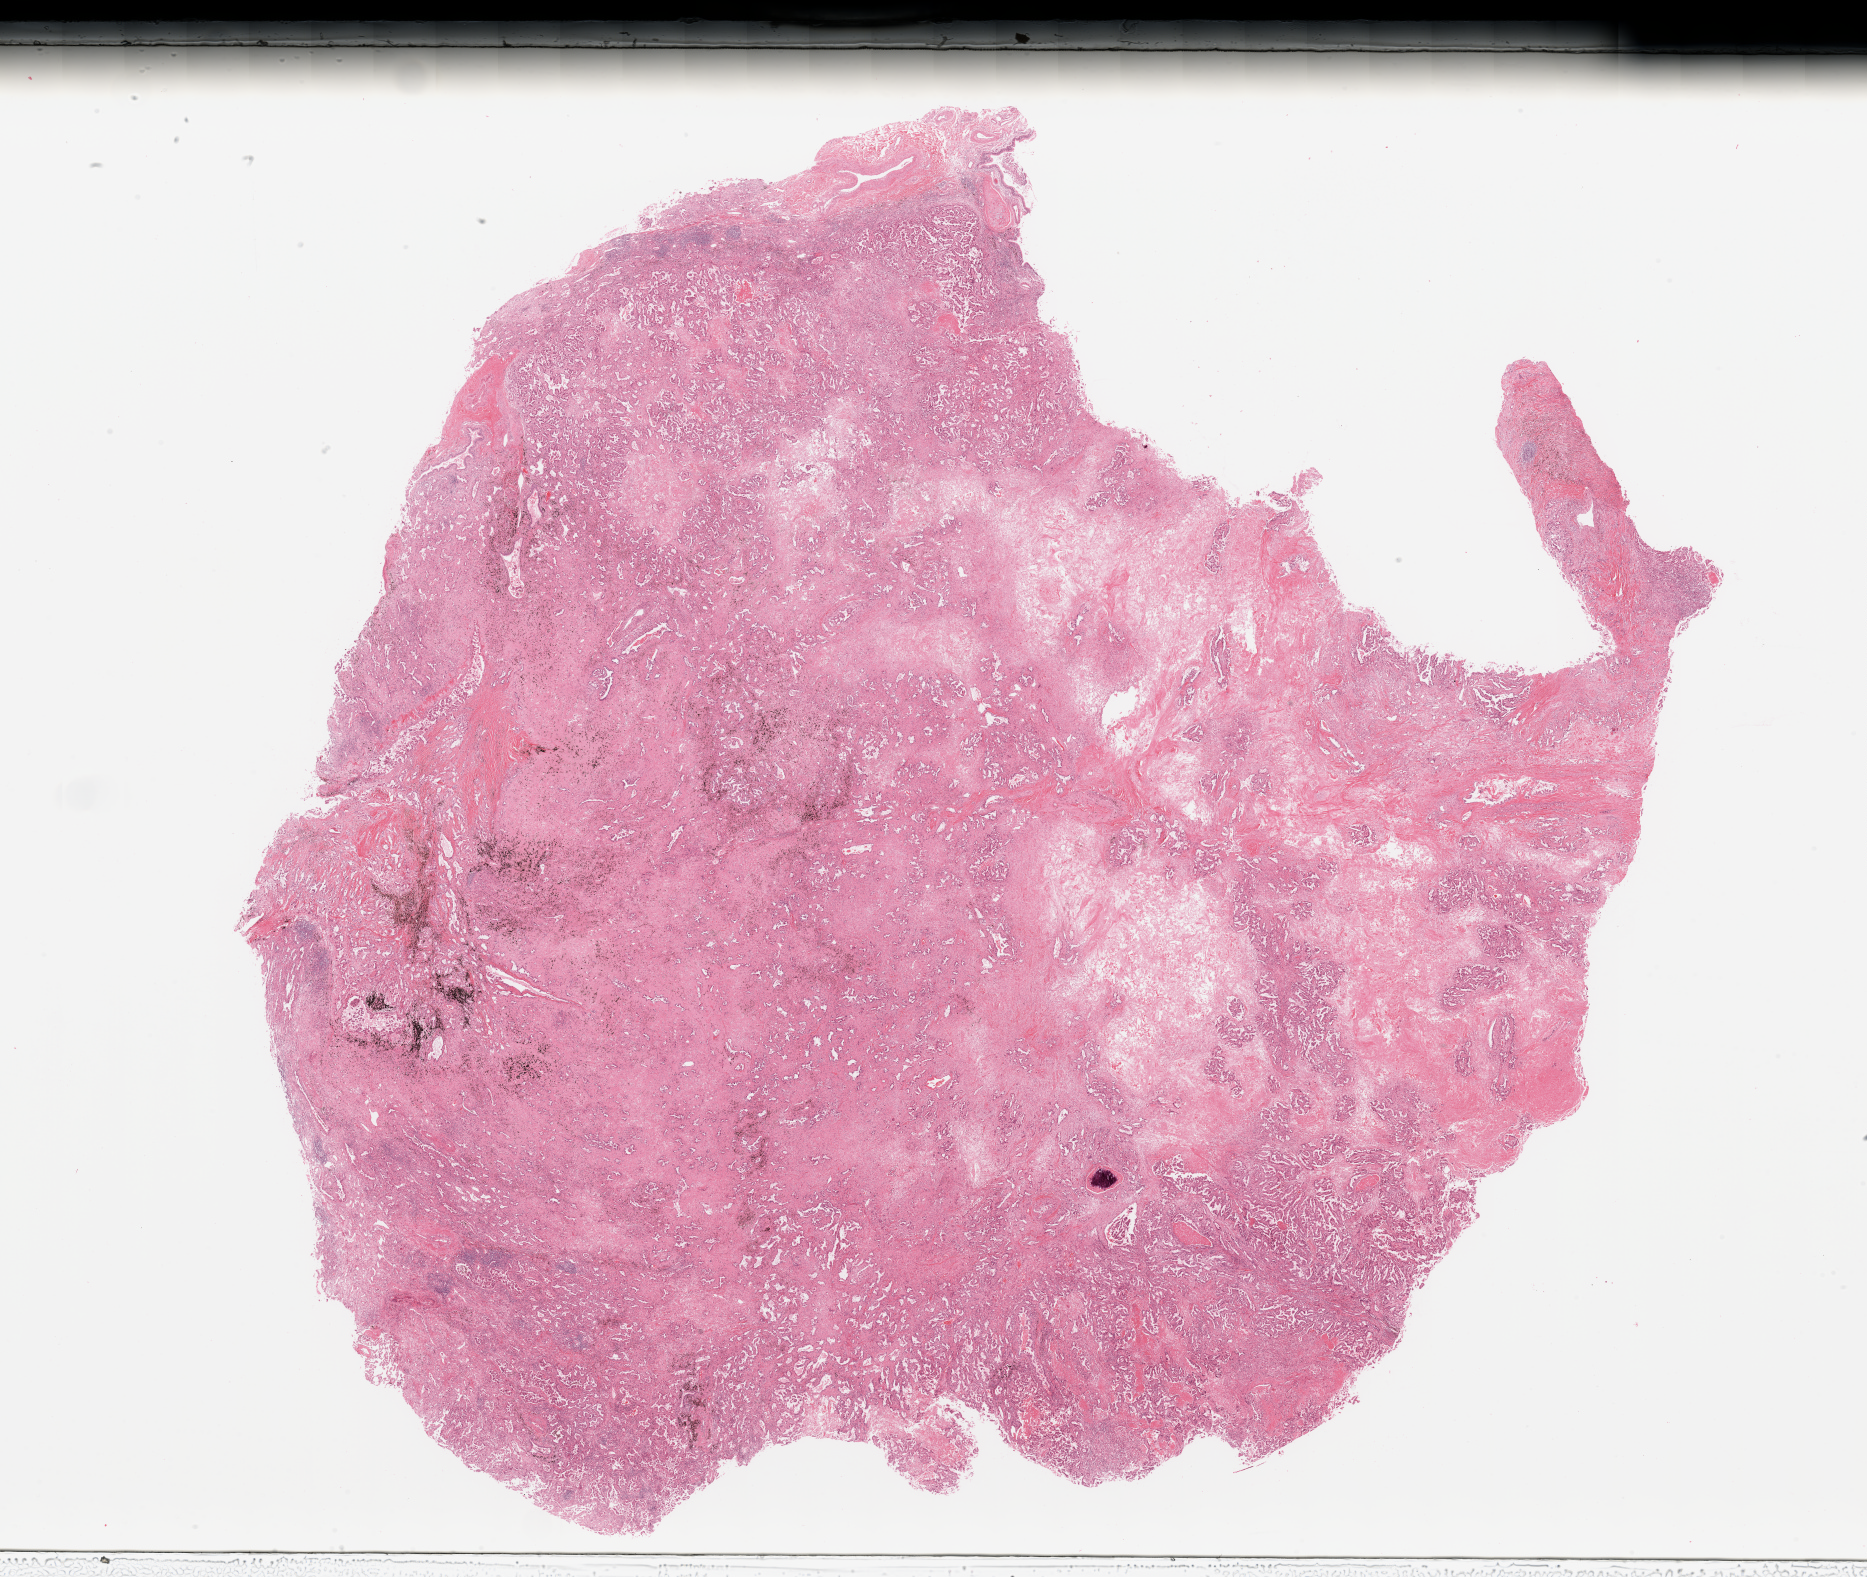
Hematoxylin and eosin (H&E) stained whole-slide image — a low-resolution overview of the entire scanned area, about 29.5 x 24.9 mm (from a 20x scan), lung, tumour tissue. 69-year-old female patient. Histologic grade: G2 (moderately differentiated).
Histologic diagnosis: Adenocarcinoma, NOS. AJCC pathologic stage: IIIA.